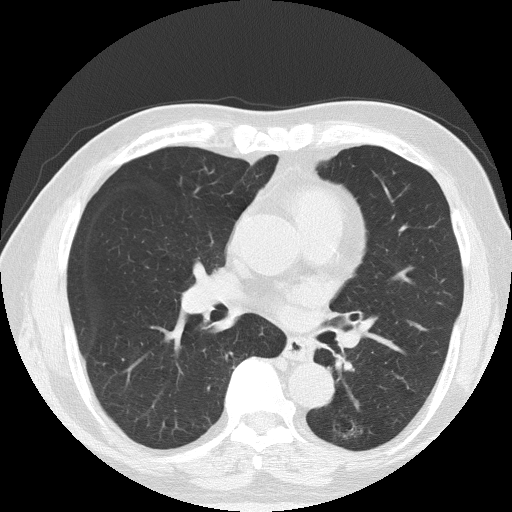
Axial slice from a low-dose chest CT screening exam. First (baseline) screen. Lung window (W 1500 / L -600 HU). 120 kVp. Male, age 71 years at enrolment. Former smoker at enrolment.
Expert-annotated lung lesion, box from (x=322, y=408) to (x=372, y=451) px. Screening reader's record for this exam: no non-calcified nodule ≥4 mm recorded. Lung cancer was diagnosed 340 days after this screen: adenocarcinoma, NOS, left lower lobe, poorly differentiated (G3), stage IA (AJCC 6th edition), 28 mm at pathology.